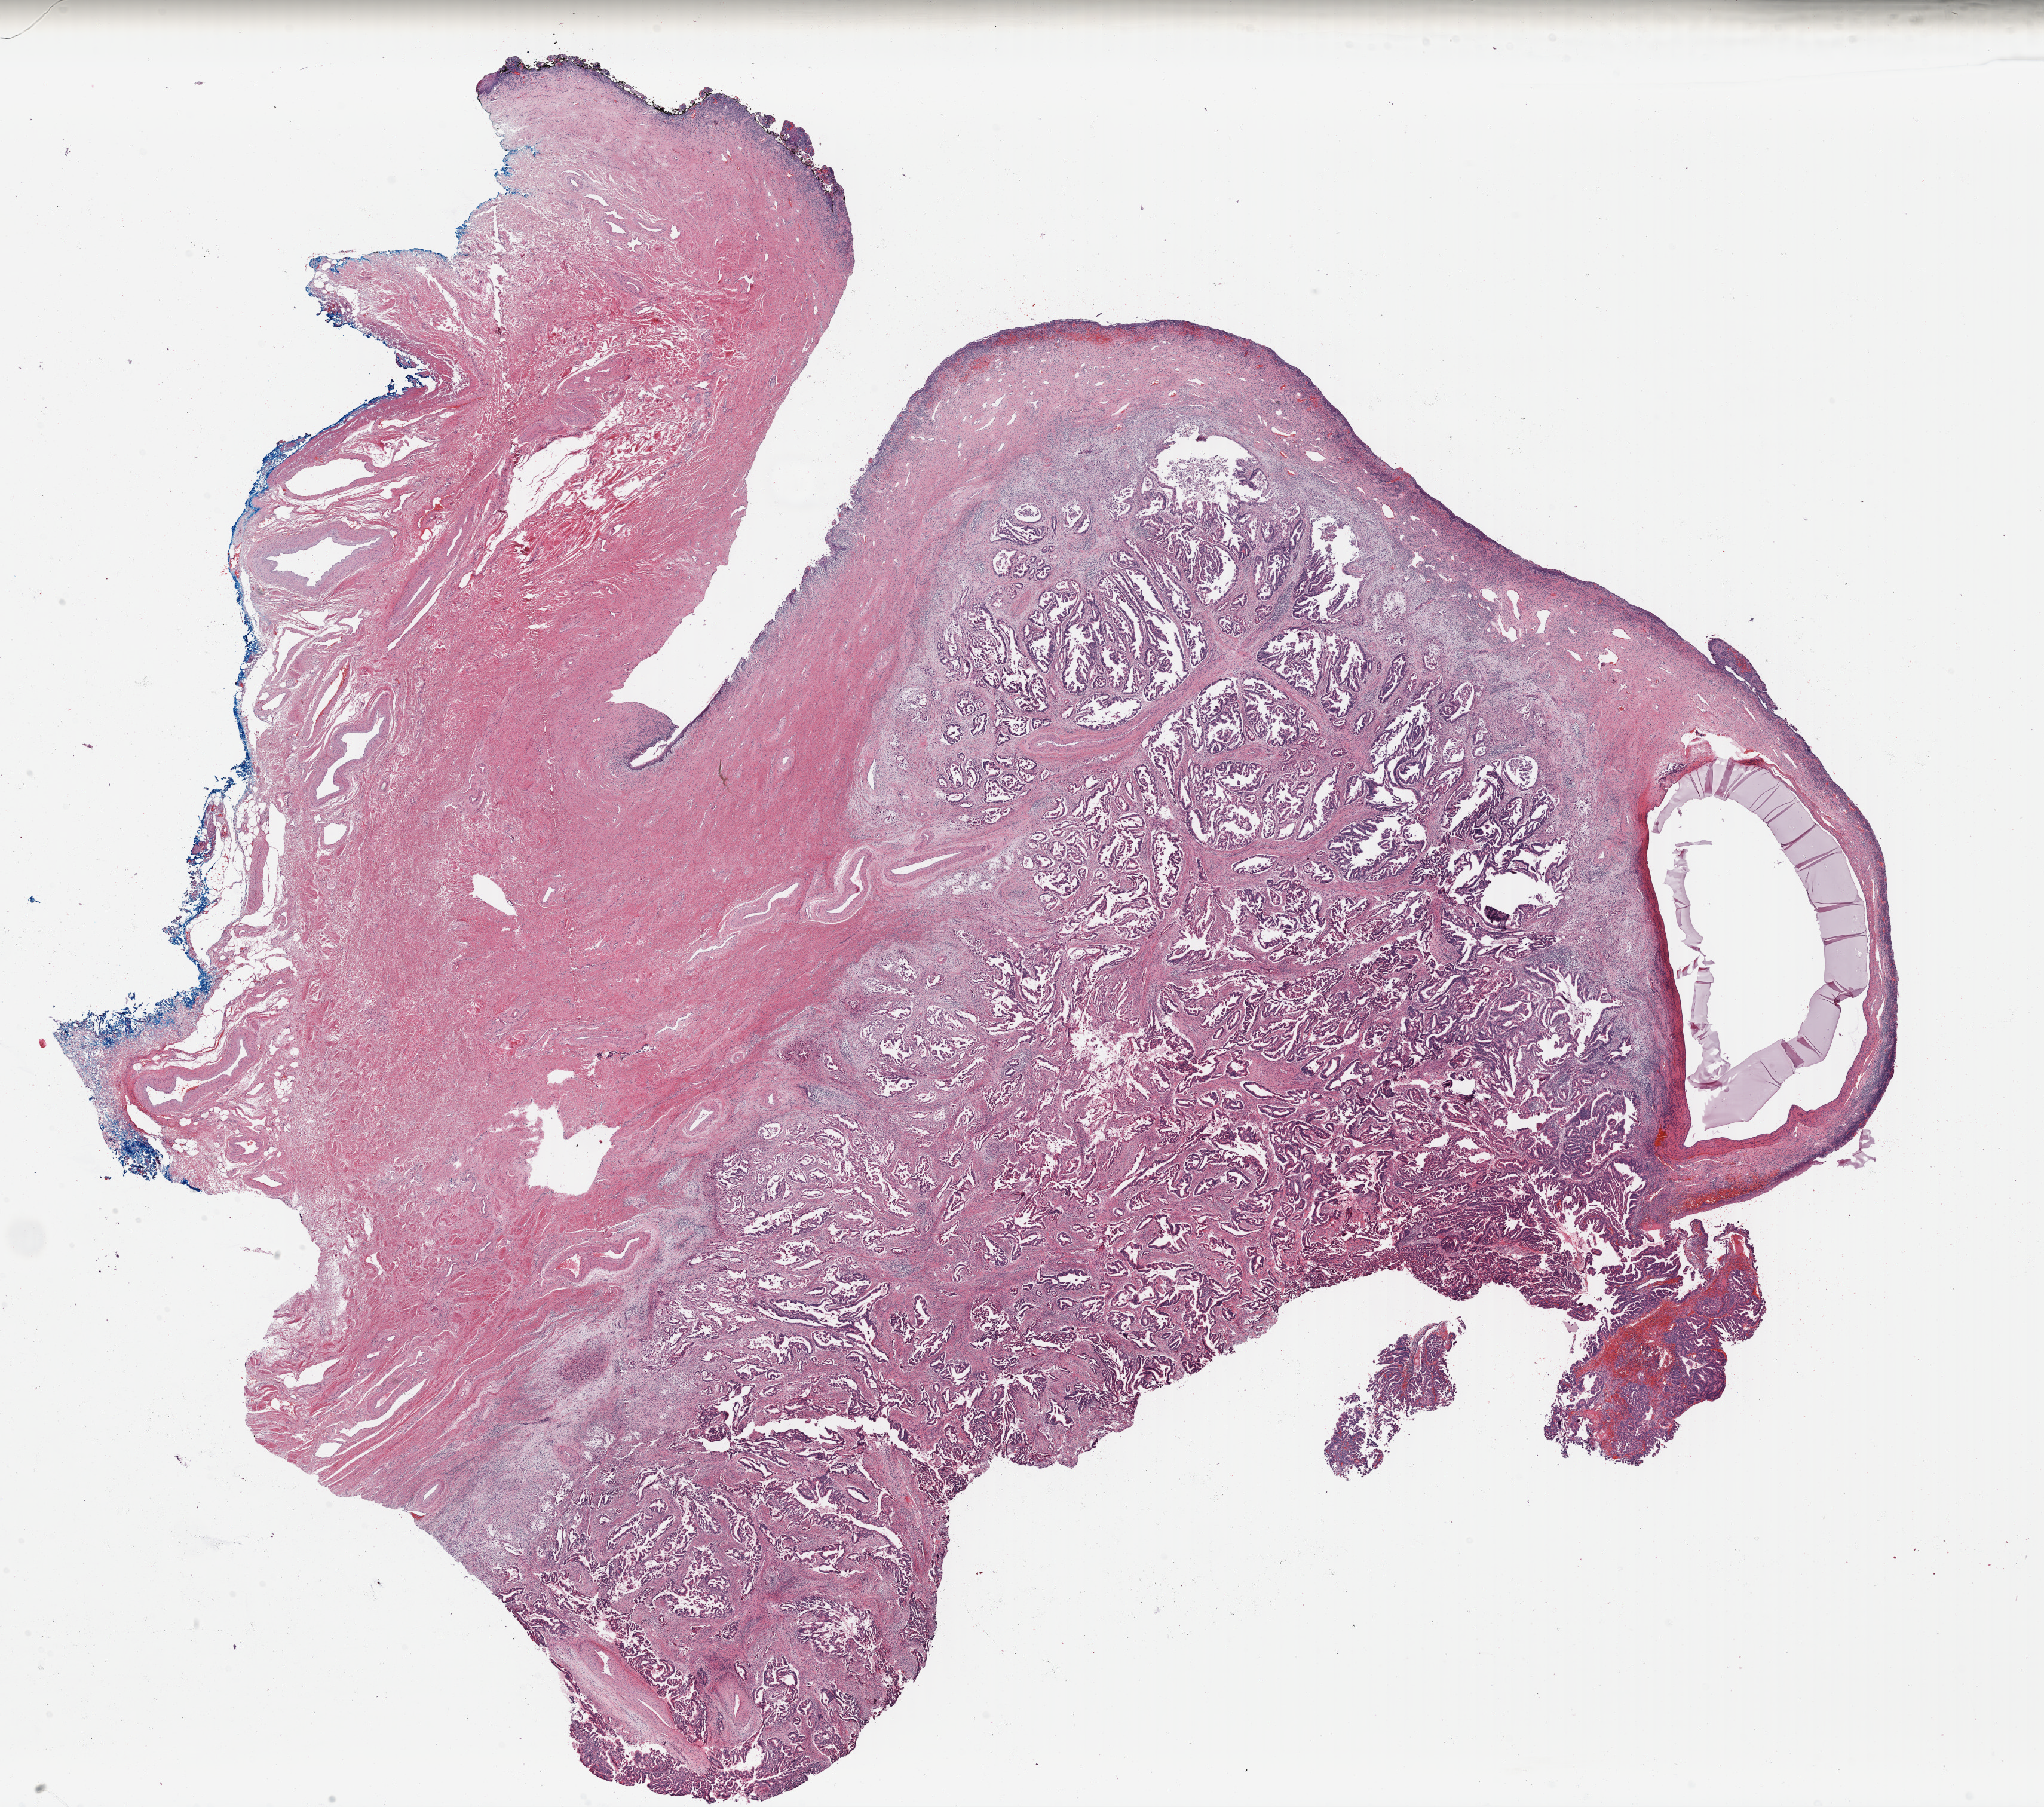
Digitized H&E tissue section (whole slide), low-resolution overview of the scanned area, about 26.9 x 23.8 mm; formalin-fixed paraffin-embedded (FFPE) diagnostic section; primary tumour sample from the cervix. Patient: female, age at initial diagnosis 53 years.
Histologic diagnosis: Adenocarcinoma, endocervical type (cervix uteri).